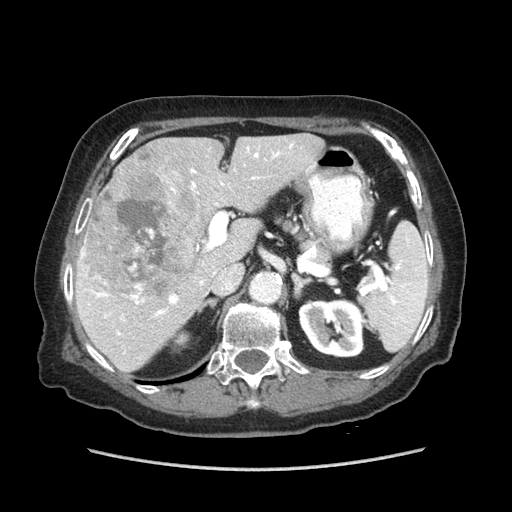
Contrast-enhanced abdominal CT (liver protocol), one axial slice; position 47 of 89 along the scan axis; reconstruction kernel STANDARD; 140 kVp; soft-tissue window (W 400 / L 40 HU); 2.5 mm slice thickness; 512 × 512 image matrix, field of view 360 × 360 mm. From the clinical record (not read from this slice): diagnosis: hepatocellular carcinoma (patient treated with transarterial chemoembolisation; whether this scan precedes or follows treatment is not stated here); TNM stage (as recorded): Stage-IIIA; Child-Pugh class: A; tumour differentiation: well differentiated; tumour nodularity: multinodular.
Annotated regions visible in this slice (semi-automatically segmented with operator editing):
- liver parenchyma outside the tumour (the mass and vessels are separate outlines, so this box may not span the whole liver): bounding box <76,134,324,372> (left, top, right, bottom; pixels)
- mass: <83,161,202,297>
- liver vessels: <81,144,312,353>